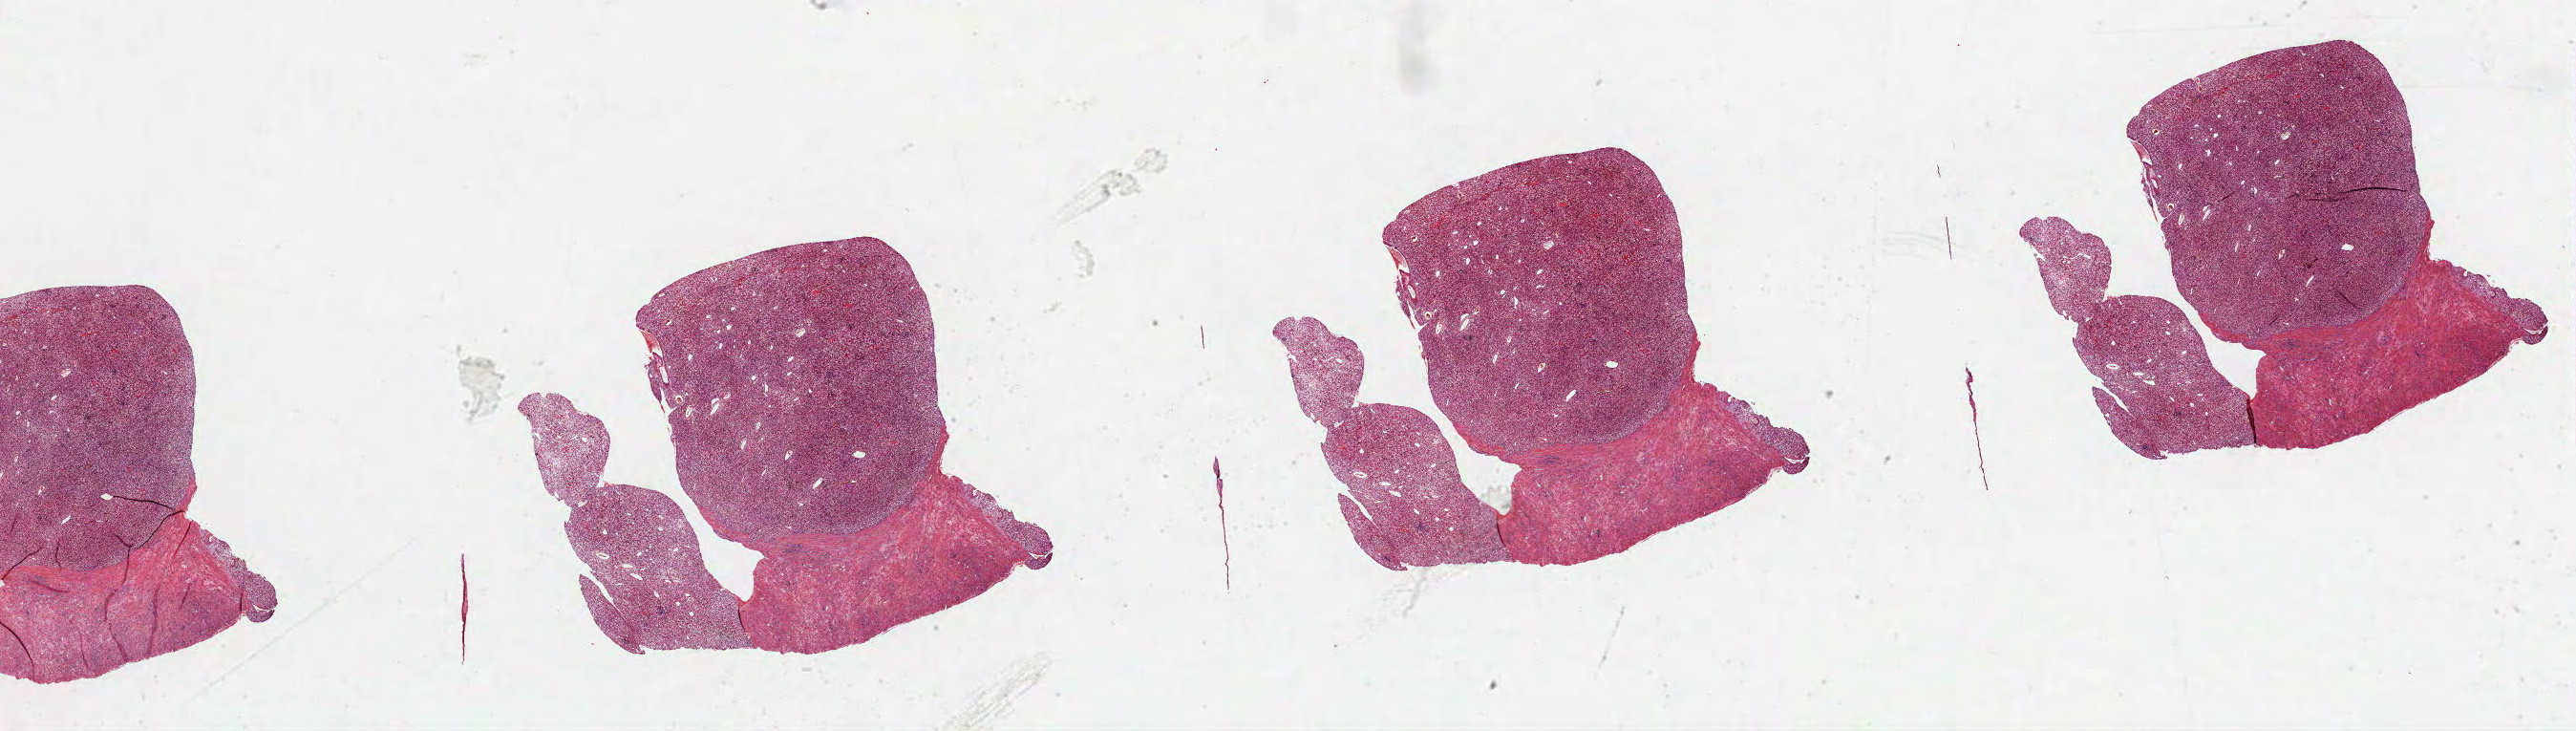
H&E-stained whole-slide image — a low-resolution overview of the entire scanned area, about 43.5 x 12.3 mm (acquisition: 40x scan), FFPE section, kidney, primary tumour sample. Male, age 61 years at initial diagnosis. Histologic grade: G2 (moderately differentiated).
AJCC pathologic stage: I. Pathologic diagnosis: Clear cell adenocarcinoma, NOS.